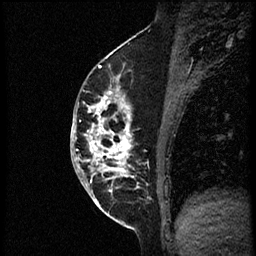
Breast MRI (dynamic contrast-enhanced), one sagittal slice. Position 28 of 56 along the scan axis. Dynamic contrast-enhanced study with each time point stored as its own series, time point 2 of 3 at this slice position (early post-contrast, ordered by acquisition time). 1.5 T. TE 4.2 ms, TR 21.3 ms. 256 × 256 image matrix, field of view 200 × 200 mm. Female patient, age 41 years. Case-level facts recorded for this patient, not image findings: setting: breast cancer imaged before/during neoadjuvant chemotherapy; receptor status: HER2-positive.
Outlined on this slice (semi-automatic segmentation, software-assisted and operator-edited):
- analysis volume of interest (the breast-tissue region the enhancement analysis was run in; not a lesion): bounding box (x1, y1, x2, y2) in pixels: (85, 73, 177, 205)
- tumour enhancement mask (voxels above the 100 % enhancement threshold inside the analysis volume of interest): (87, 76, 134, 205)